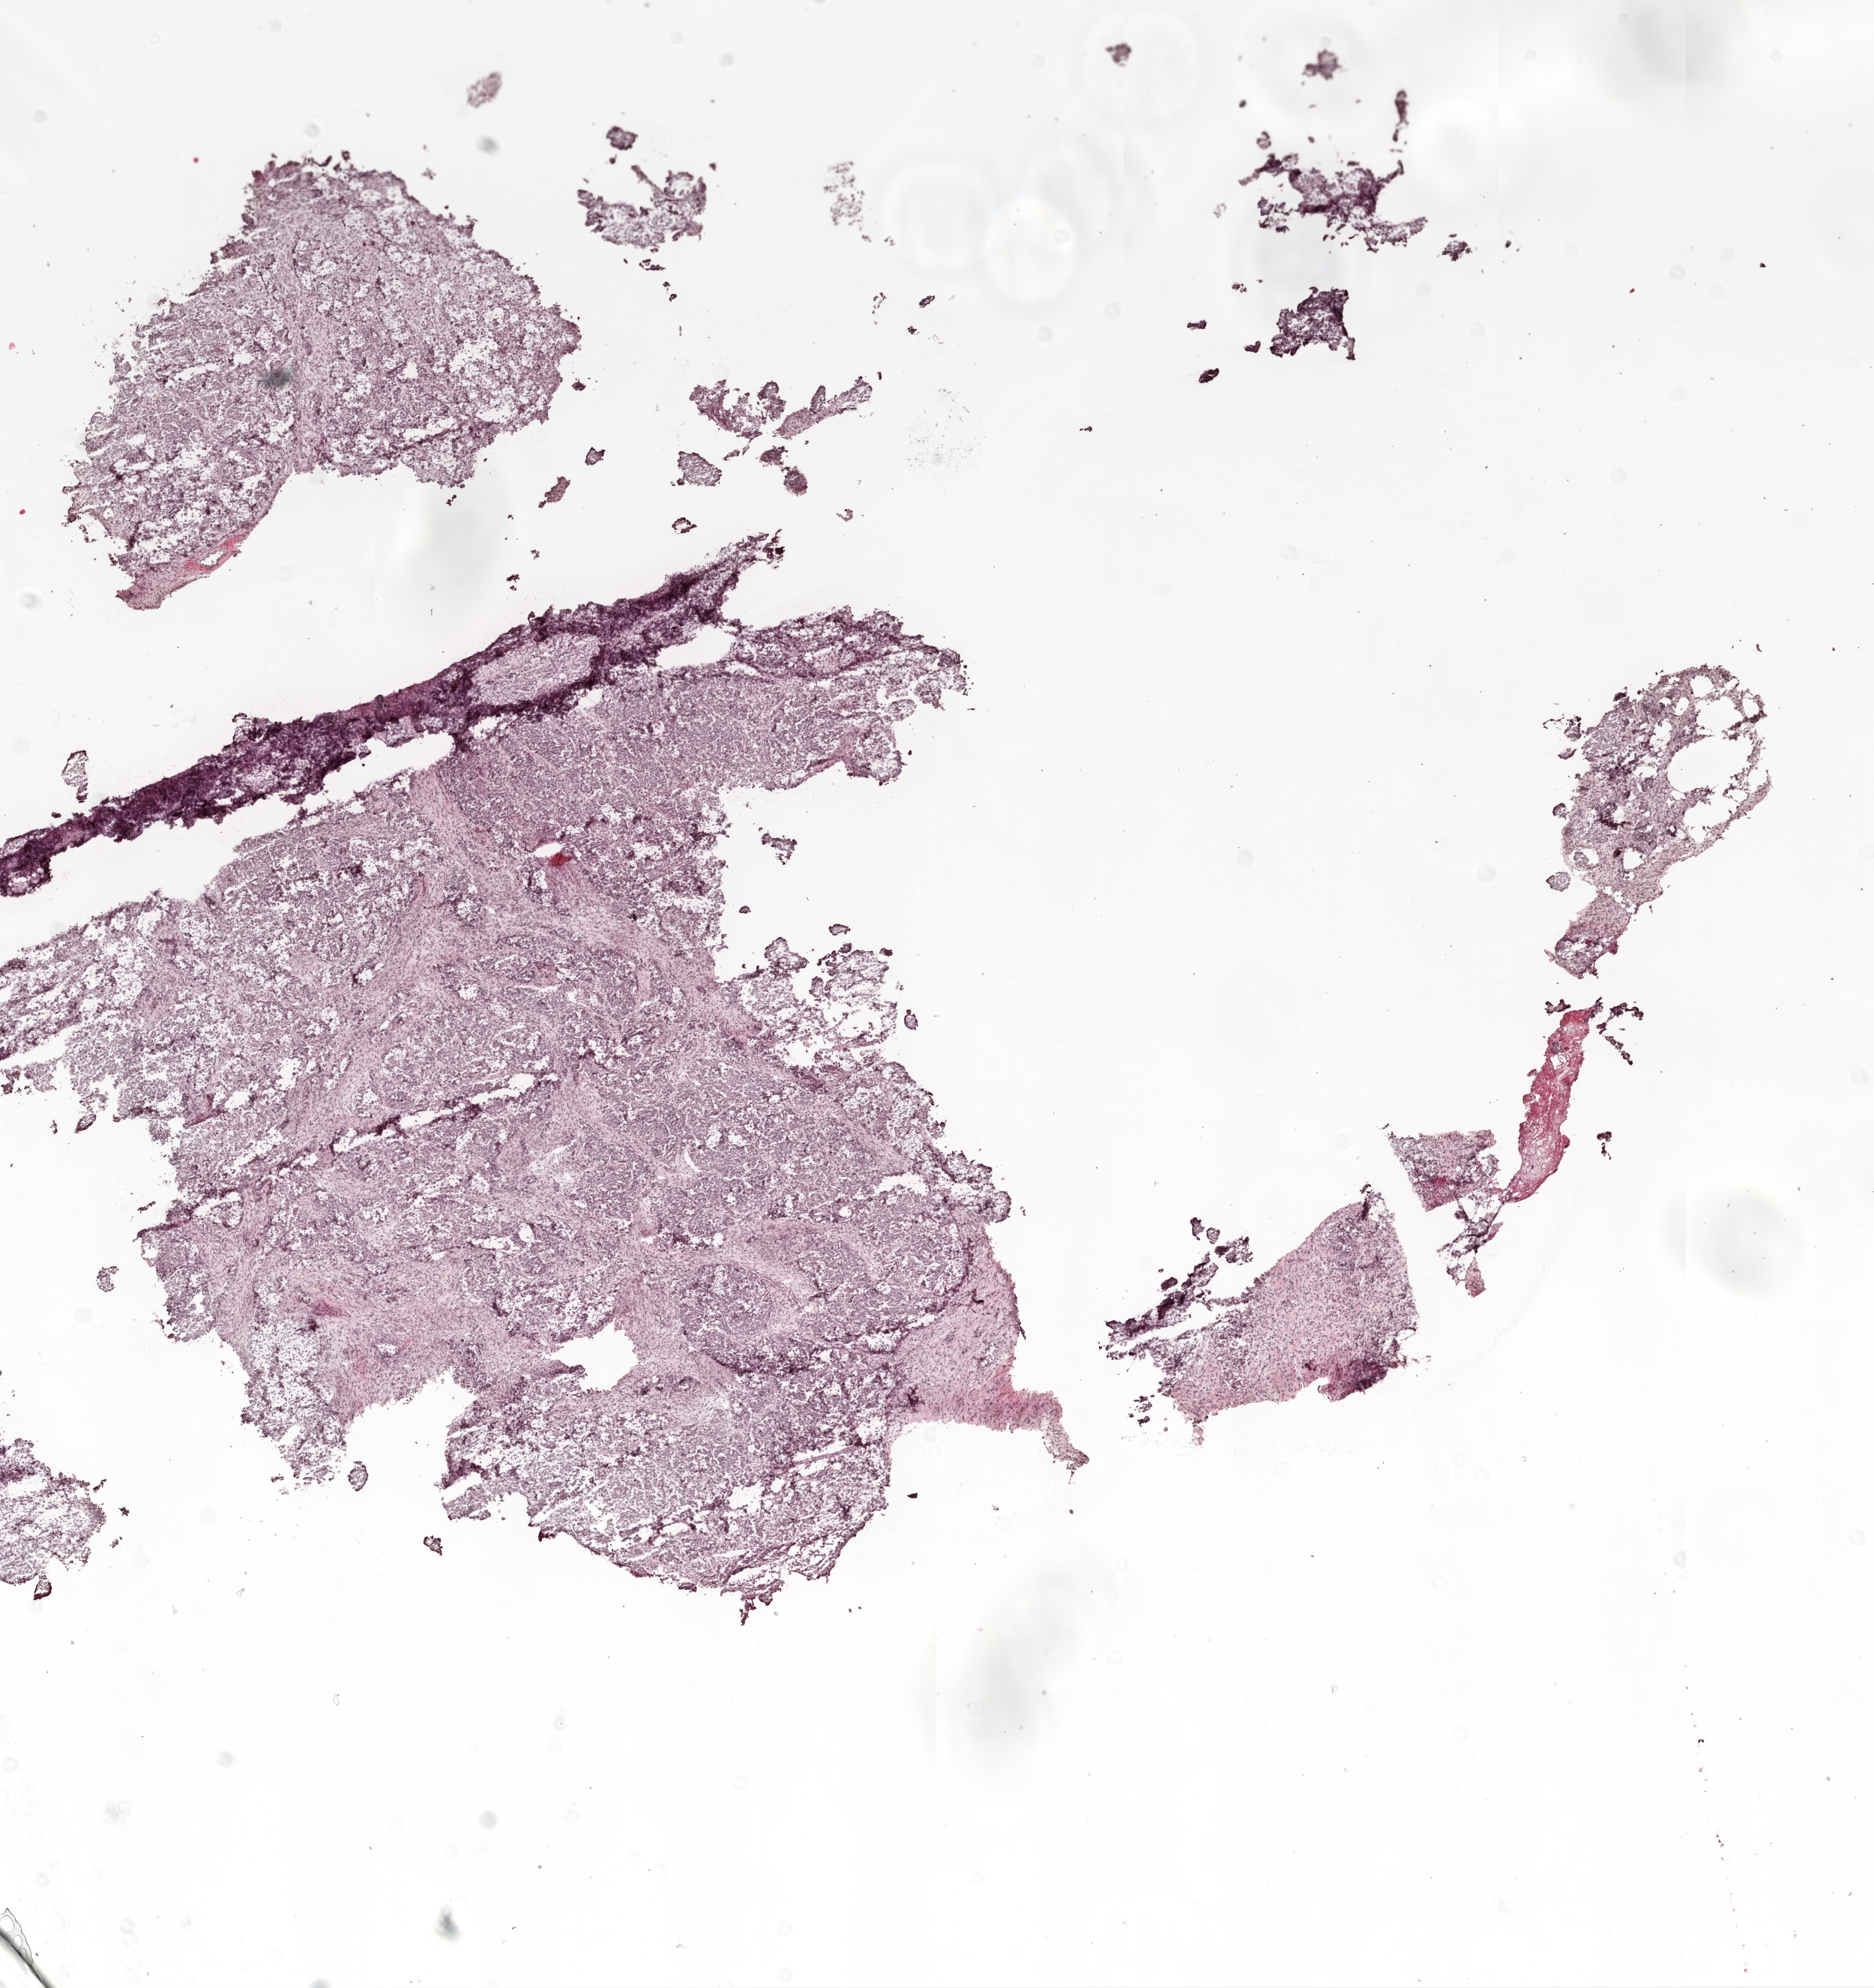
Digitized H&E-stained tissue section (whole slide) — low-resolution overview of the scanned area, about 10.0 x 10.6 mm; frozen section from the top of the tissue portion; sample: primary tumour, ovary. Female patient; age at initial diagnosis 67 years.
Histologic diagnosis: Serous cystadenocarcinoma, NOS.